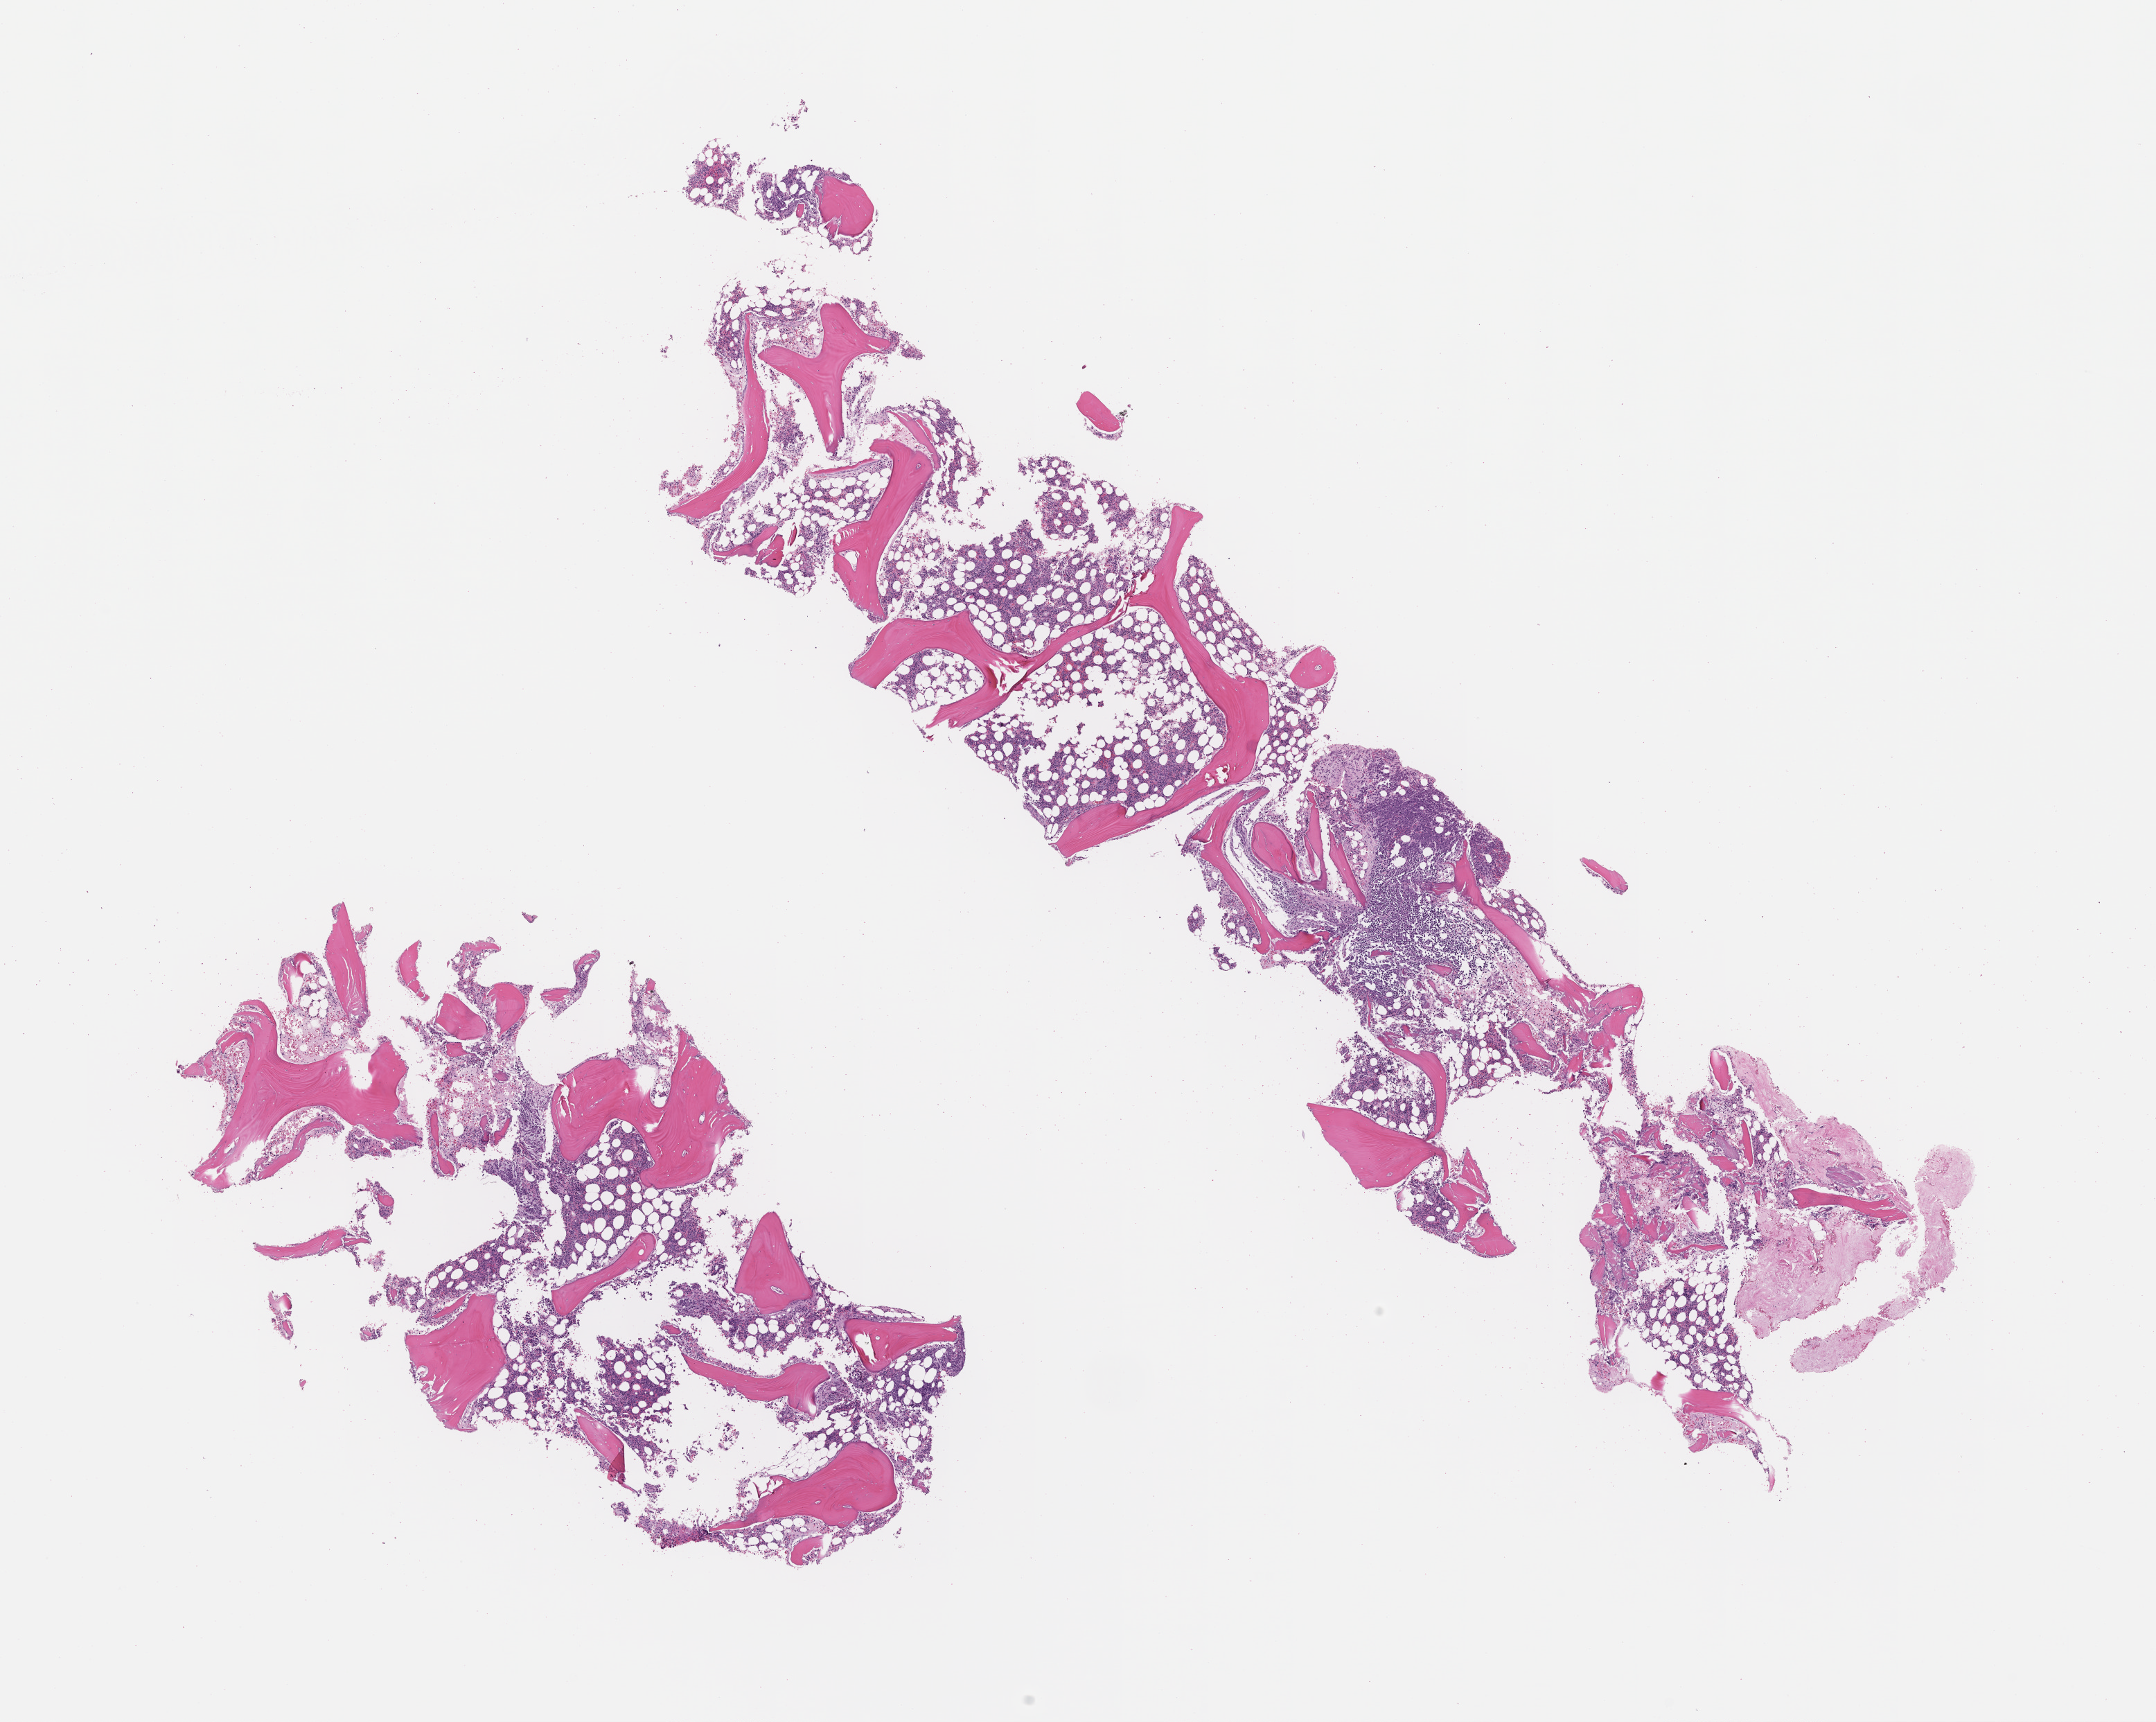
Digitized hematoxylin and eosin (H&E)-stained section, a low-resolution overview of the entire scanned area, about 12.6 x 10.0 mm. Formalin-fixed, paraffin-embedded (FFPE) tissue. Site: bone marrow. Female patient.
• this section: primary tumor
• diagnosis: Plasma Cell Myeloma